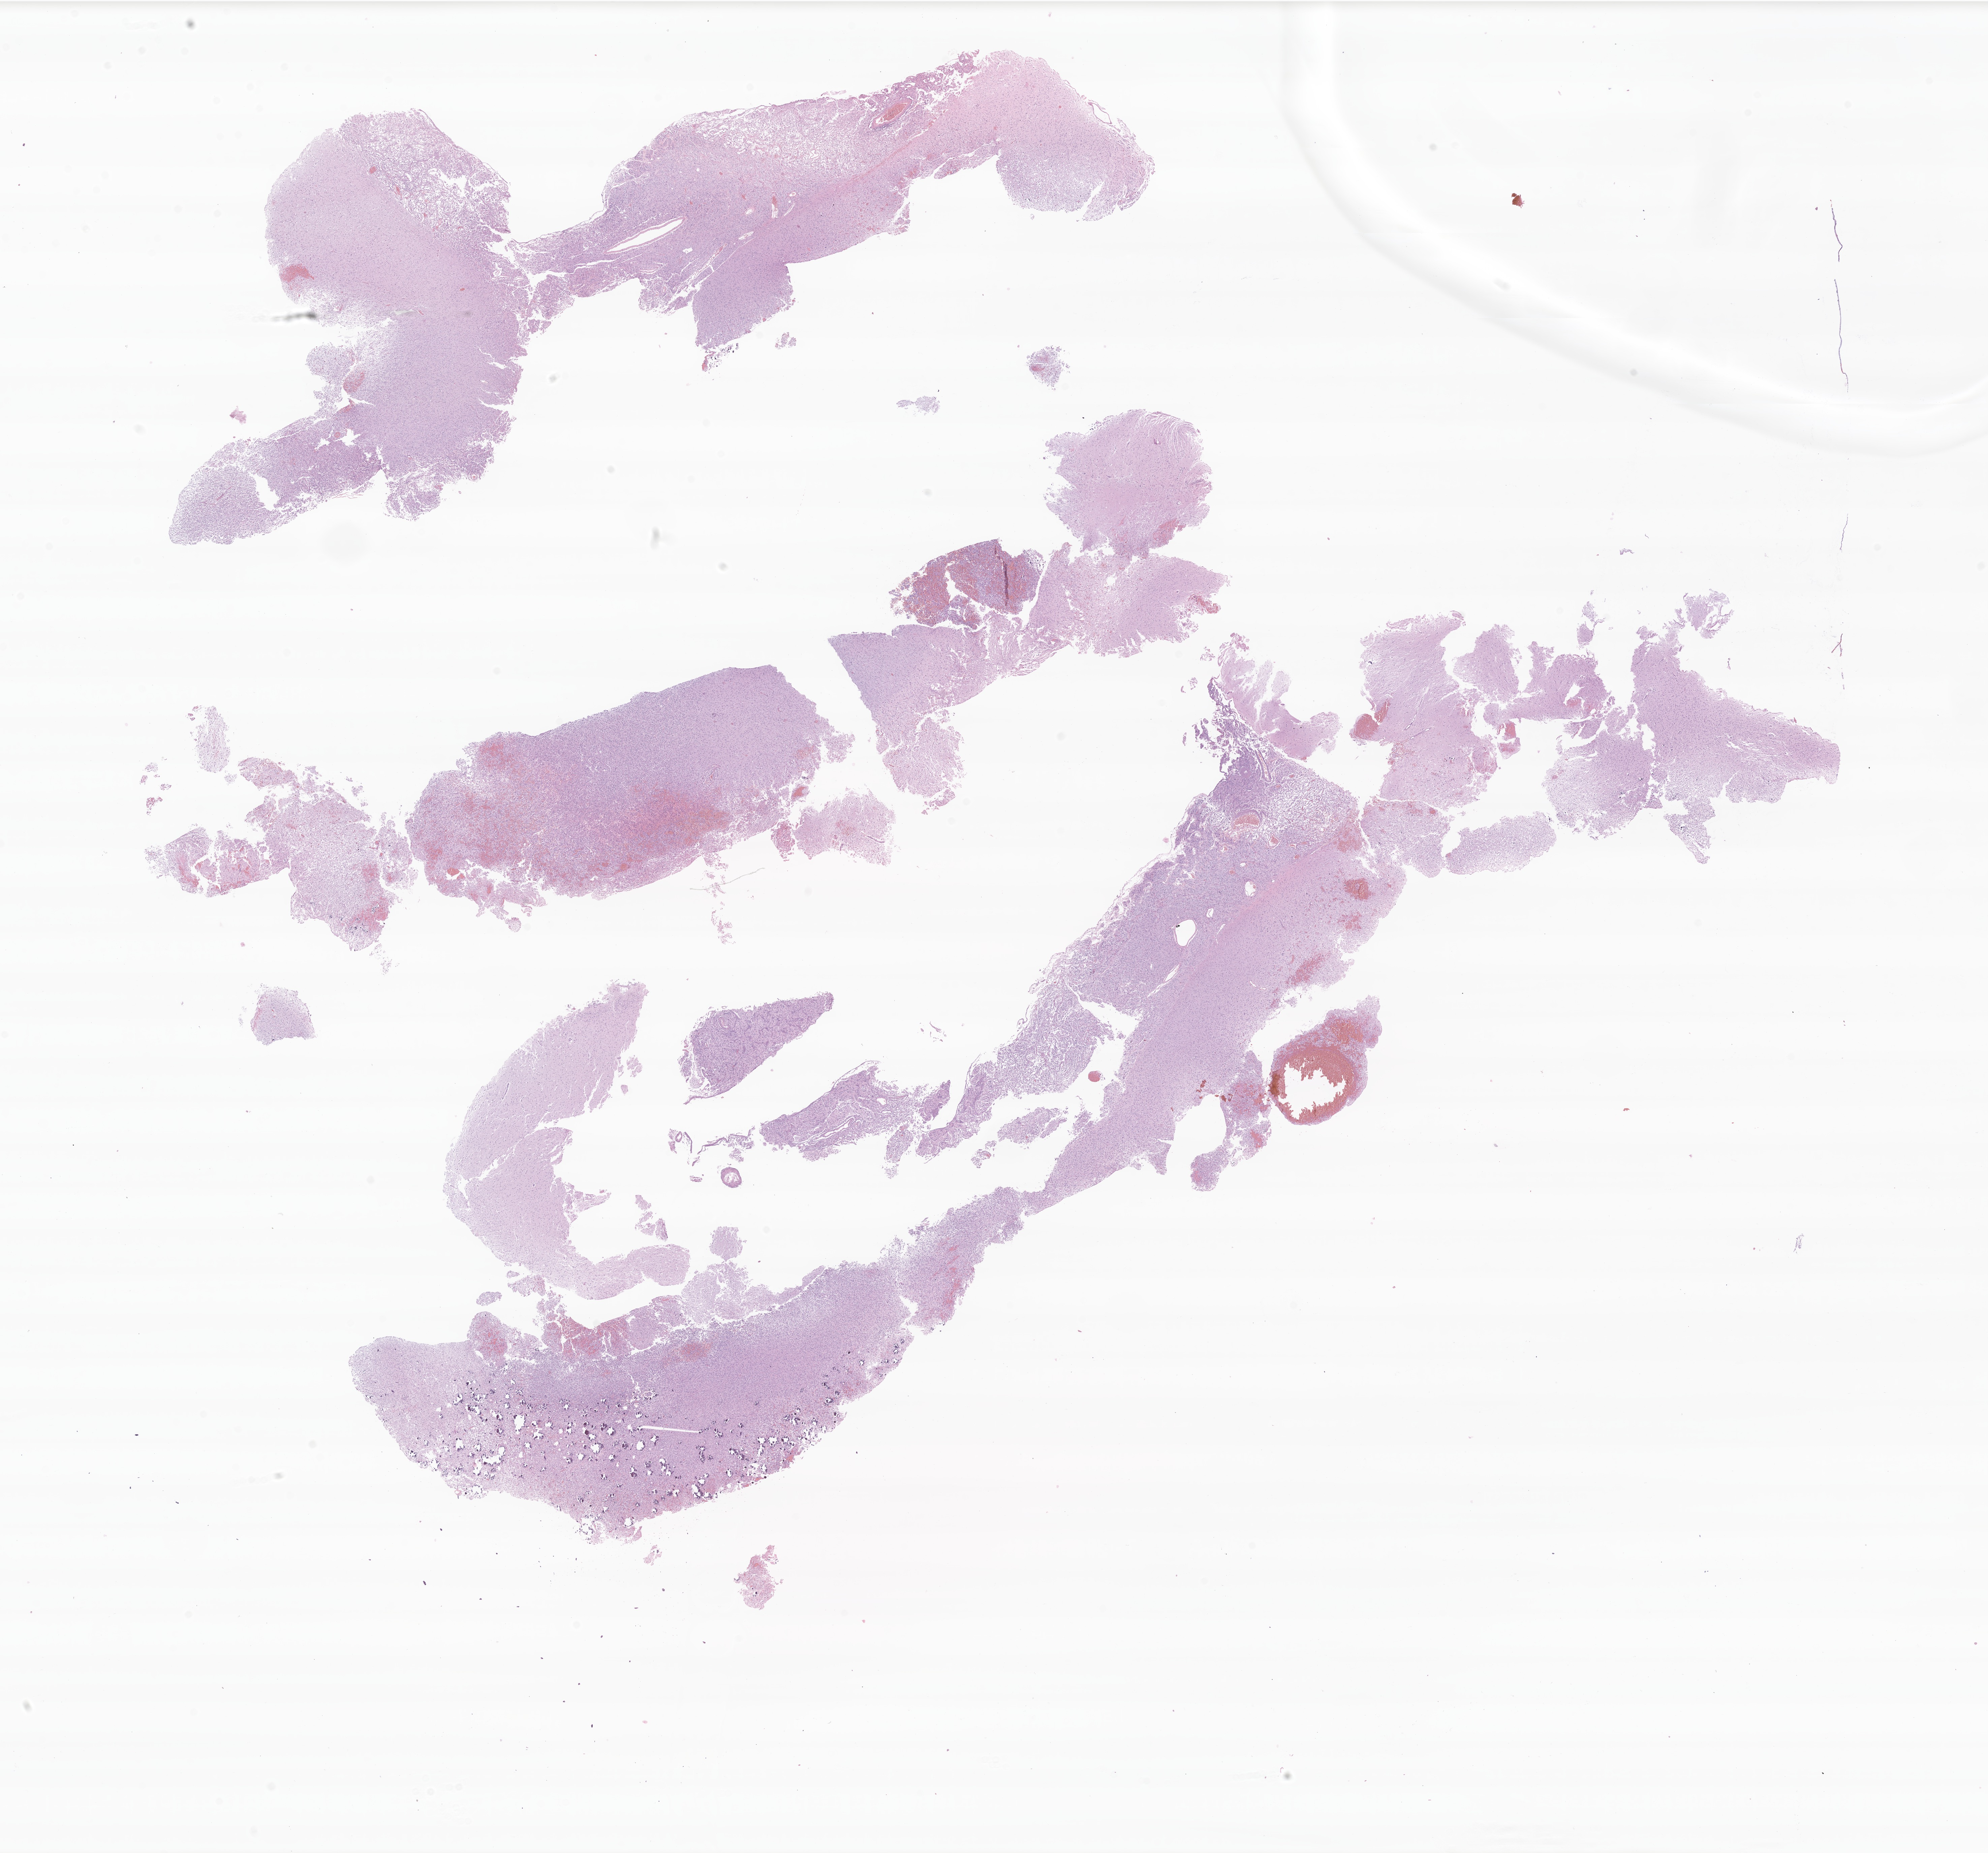
Whole-slide image, haematoxylin and eosin stain of tumor tissue from the brain — whole scanned area (about 24.9 x 23.2 mm) shown as a low-resolution overview; formalin-fixed, paraffin-embedded (FFPE) tissue. Male patient, age 107 months (8 years 11 months).
Diagnosis (ICD-O-3 morphology term): Pleomorphic xanthoastrocytoma, NOS.